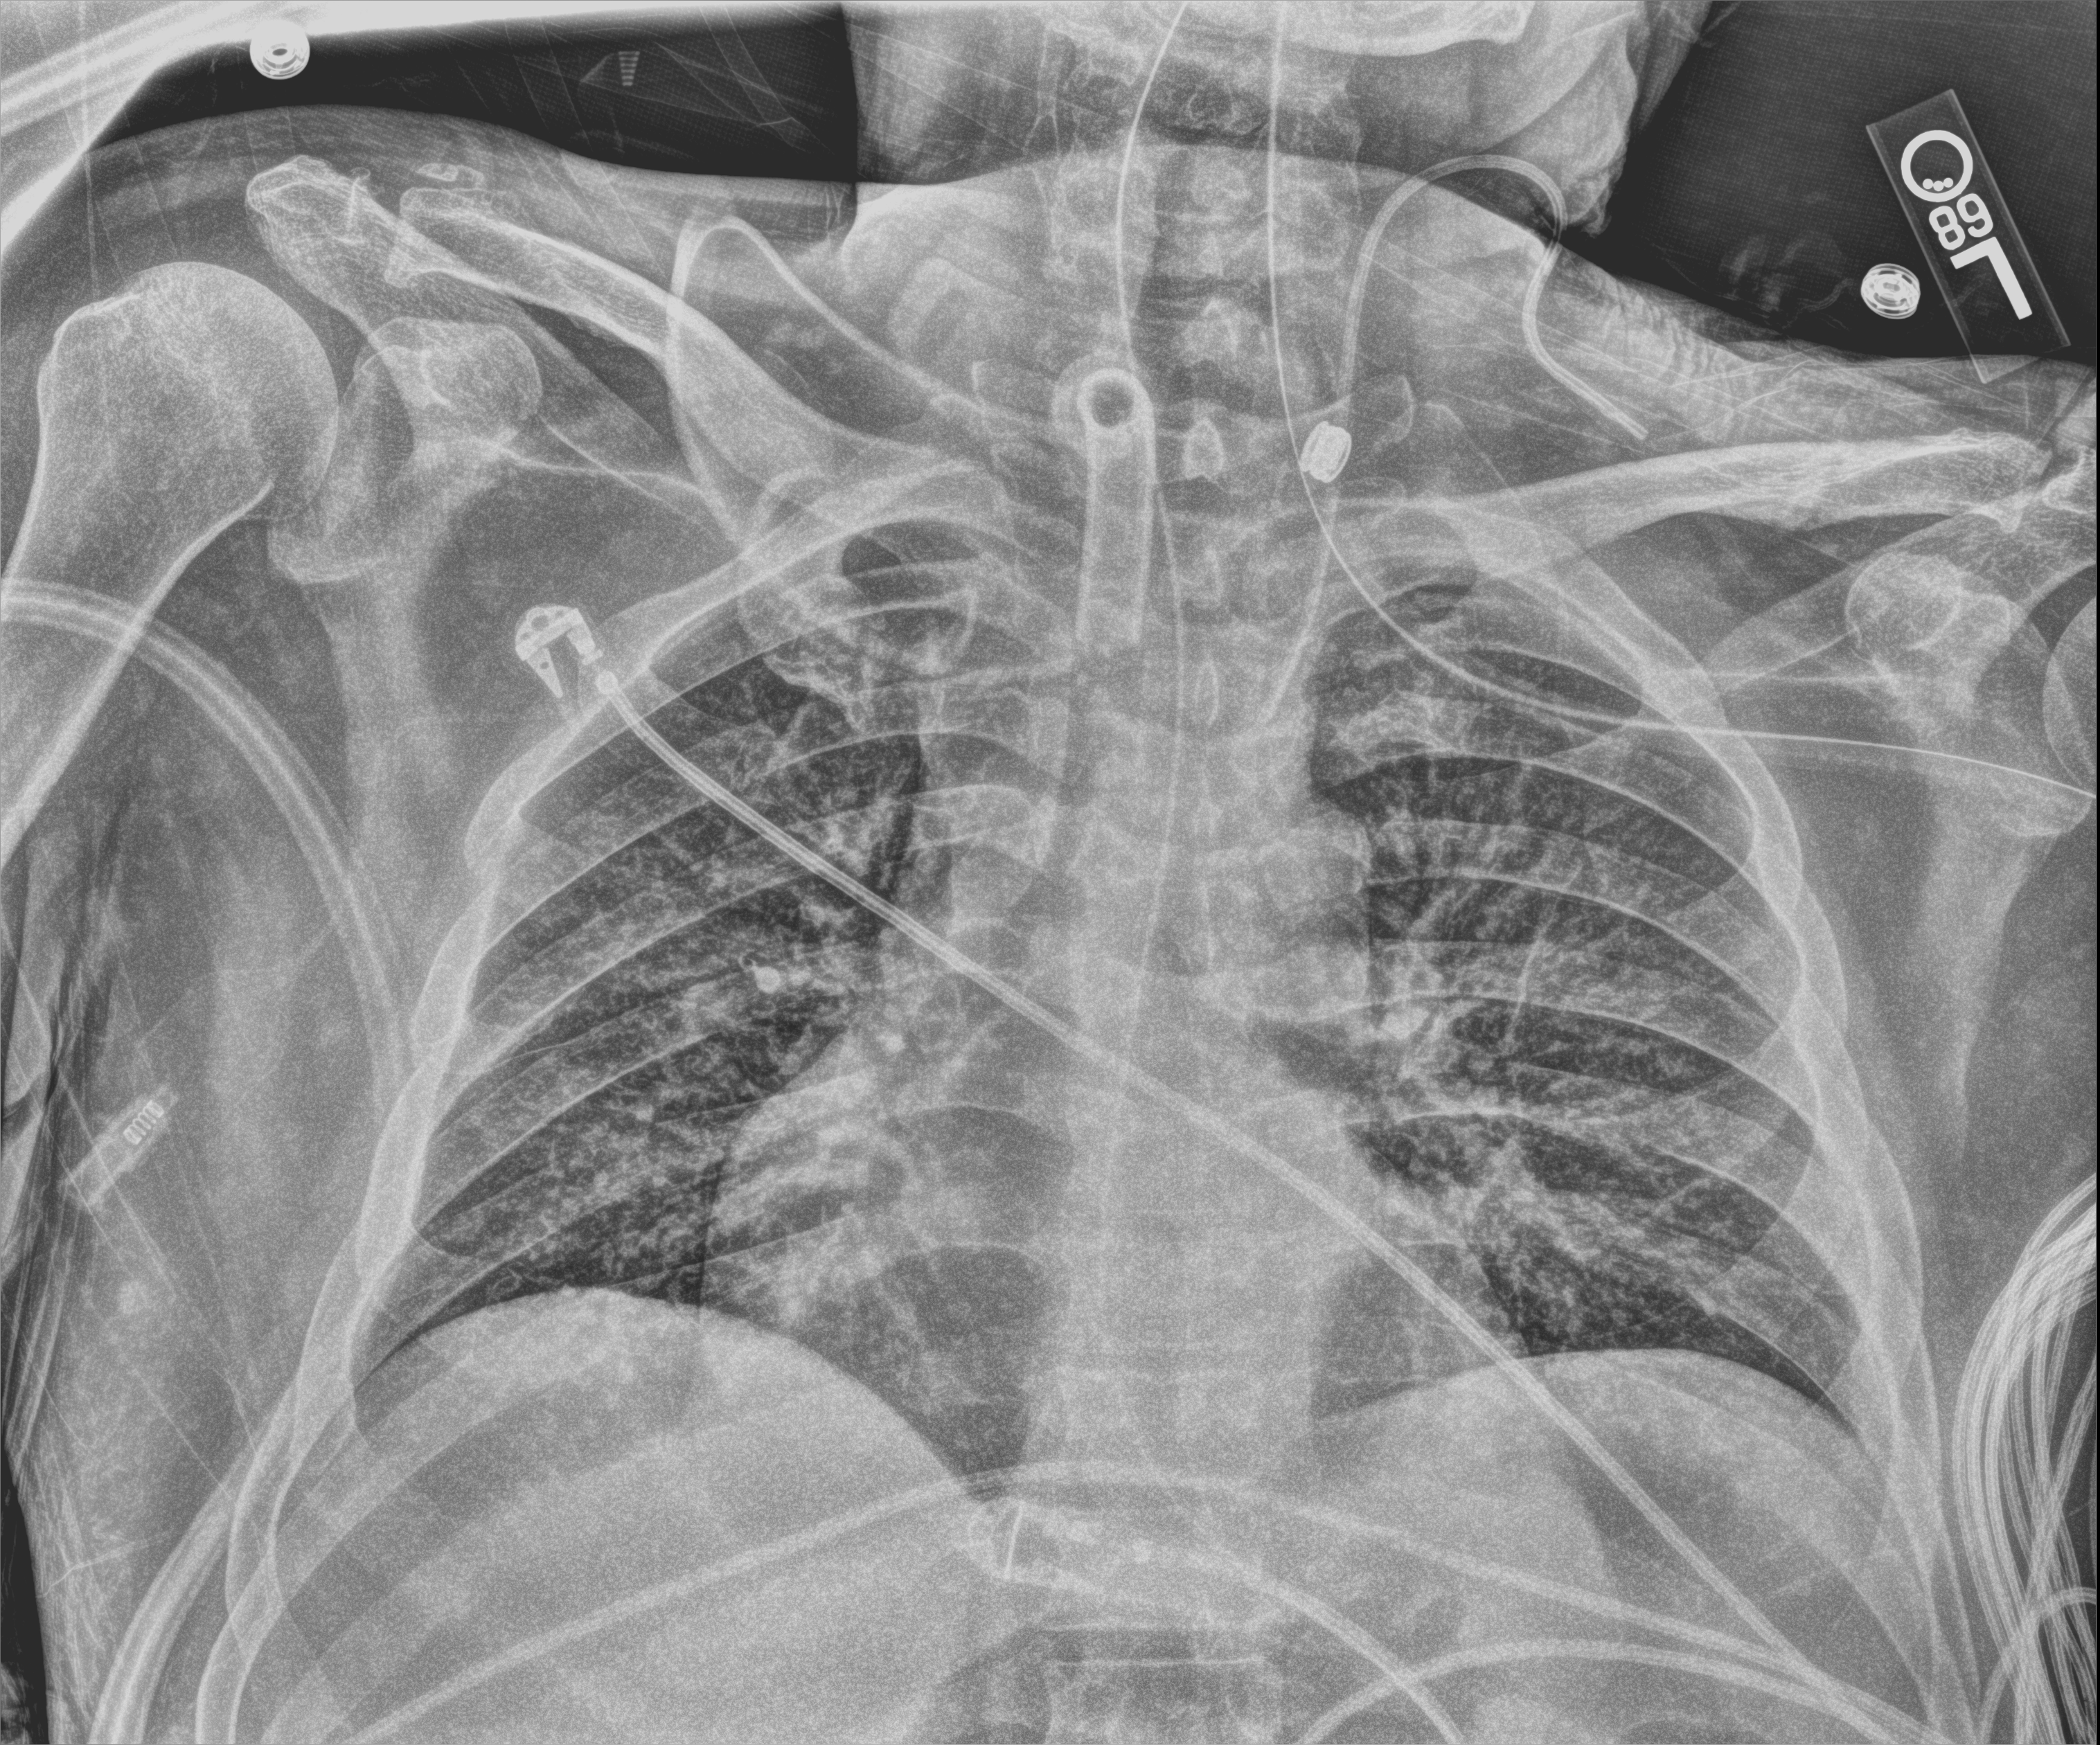
Chest X-ray (portable). Male patient hospitalised with COVID-19, age 18–59 years.
Admission-level facts for this patient (not findings on this image; timing relative to this image not recorded):
- mechanically ventilated during this hospital stay: yes
- admitted to intensive care during this hospital stay: yes